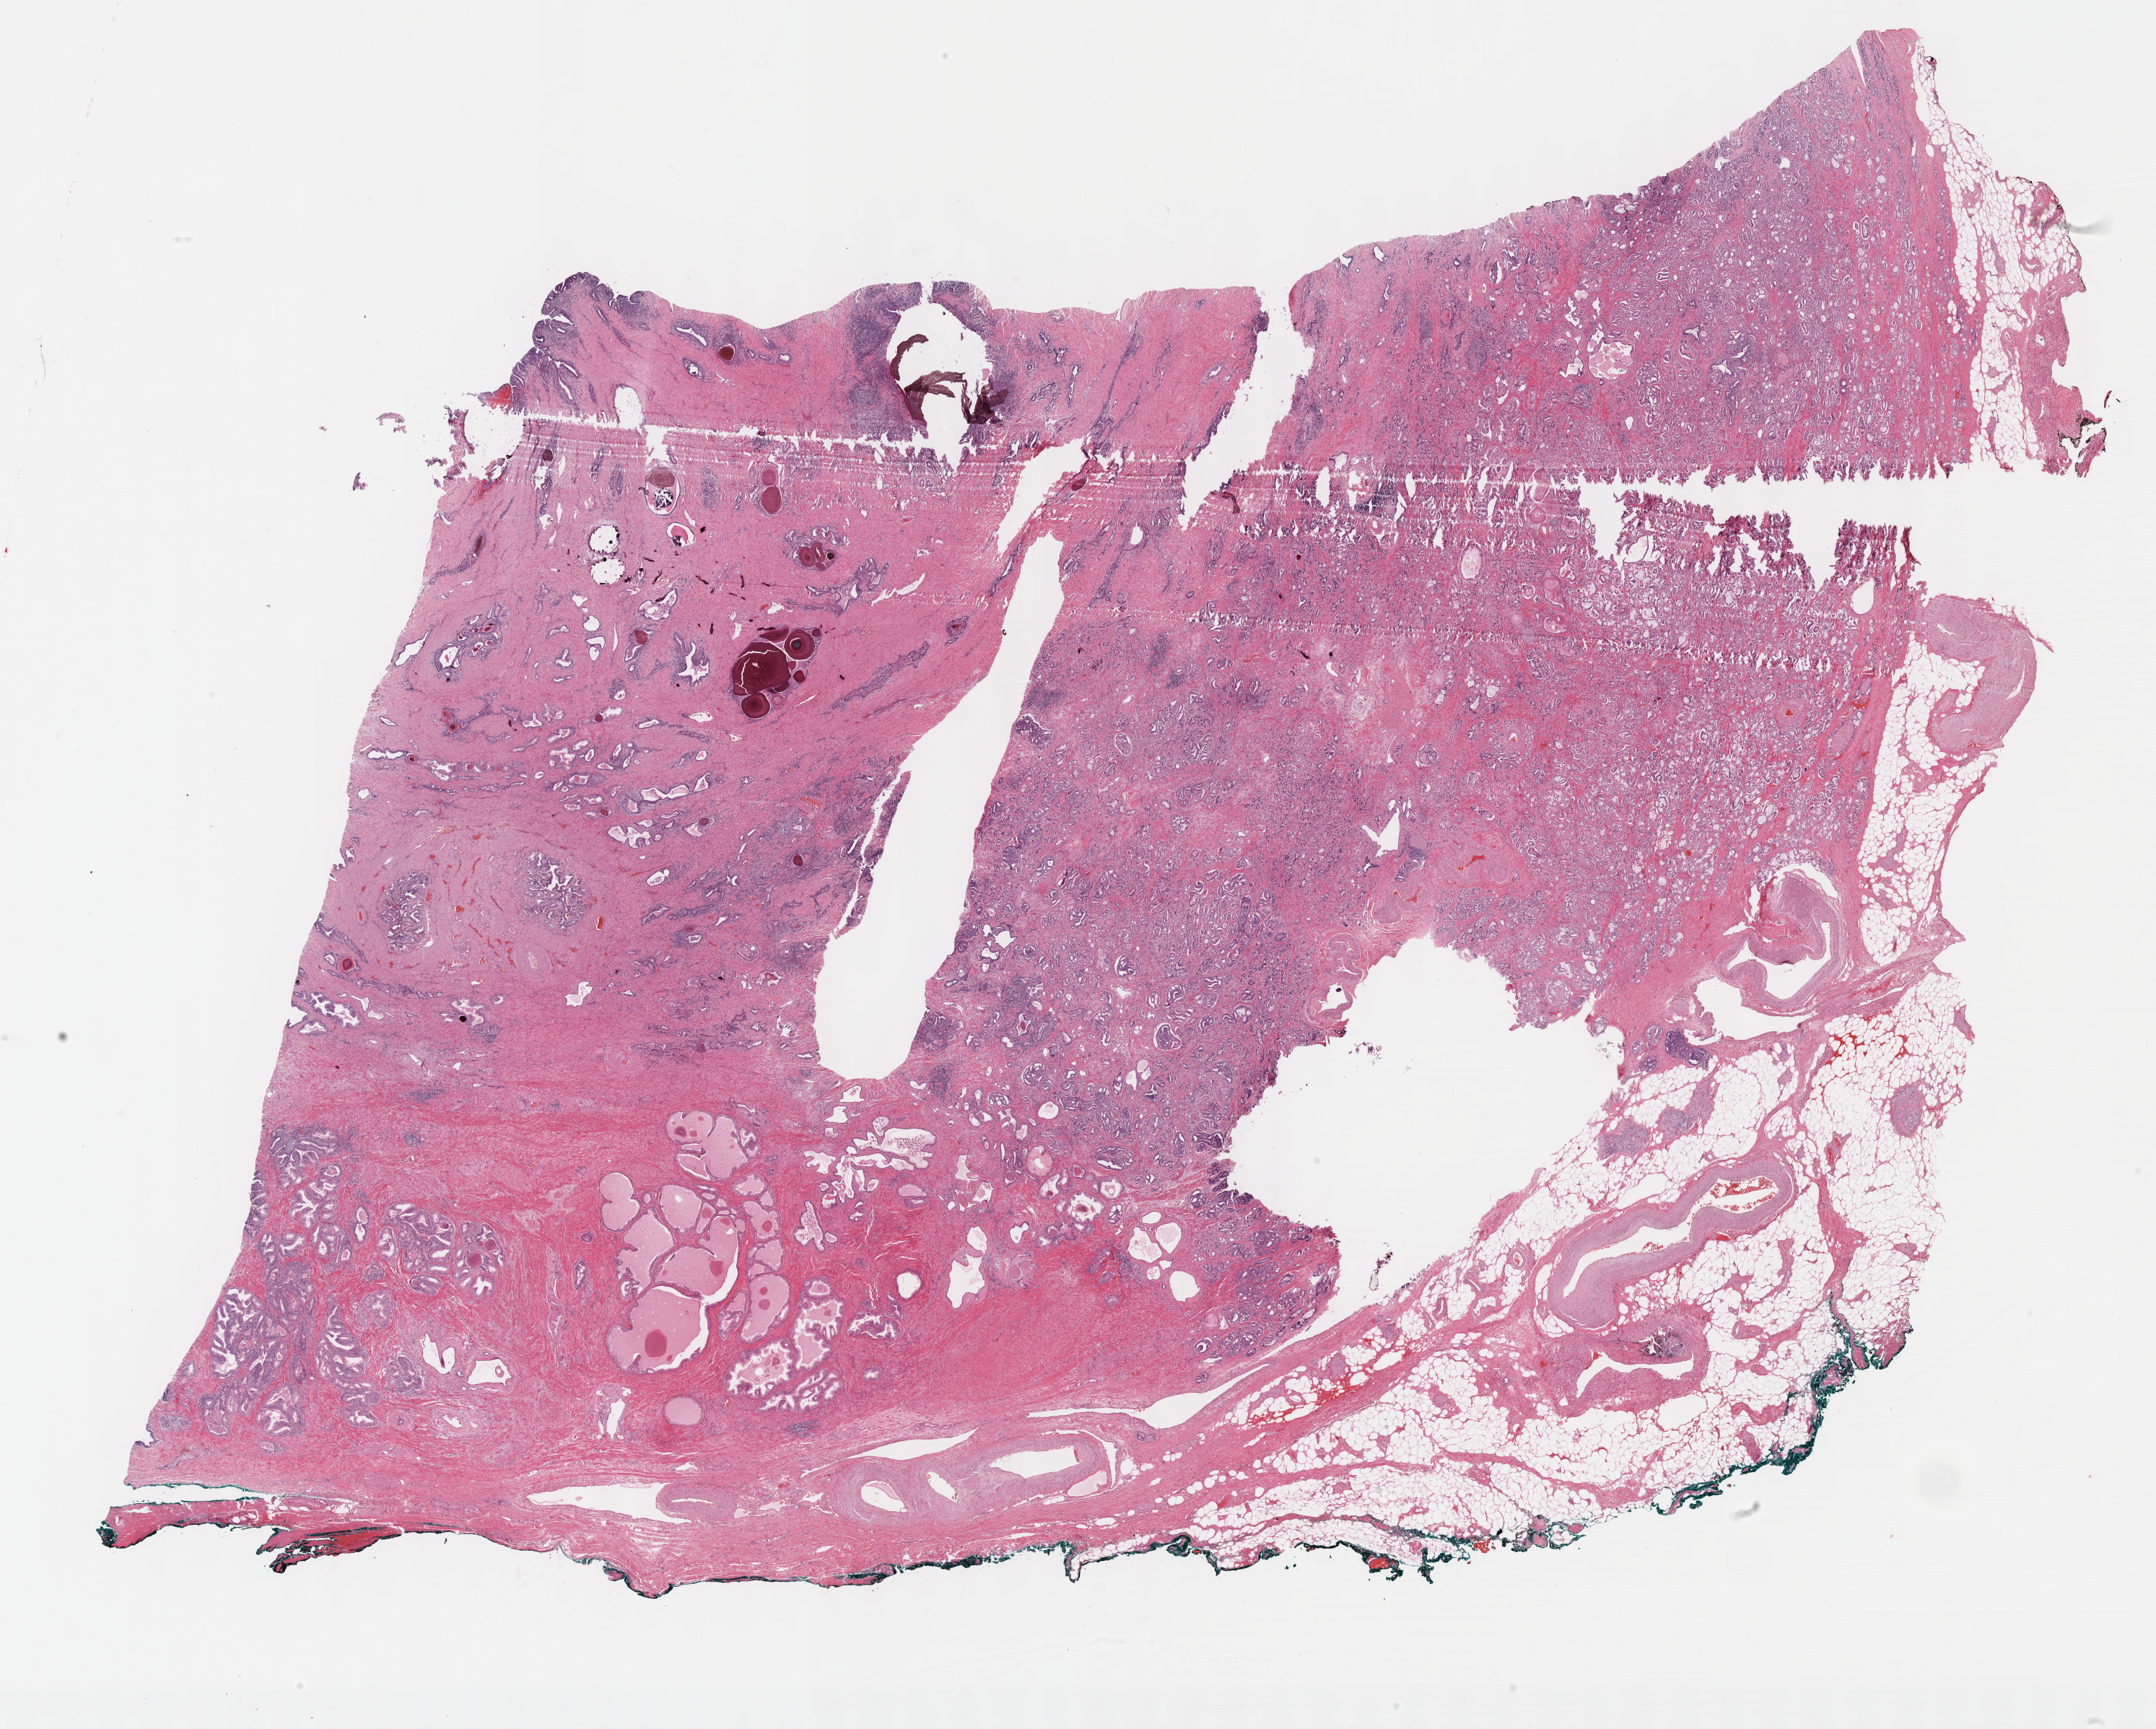
H&E-stained whole-slide image — low-resolution overview of the scanned area, about 24.2 x 19.4 mm (acquisition: 40x scan), formalin-fixed paraffin-embedded (FFPE) diagnostic section, primary tumour sample from the prostate. Male, age 64 years at initial diagnosis. Gleason score: 7 (4+3).
Laterality: left. Diagnosis: Adenocarcinoma, NOS (prostate gland).